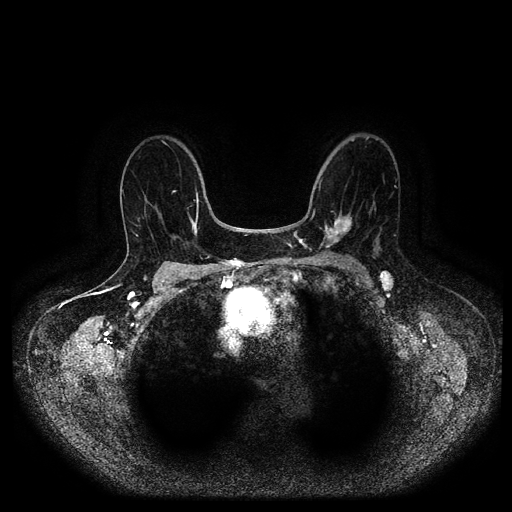
Breast MRI (dynamic contrast-enhanced, multi-phase), one axial slice. Position 59 of 116 along the scan axis. Dynamic contrast-enhanced series, time point 2 of 5 at this slice position (early post-contrast). 1.5 T. TE 2.6 ms, TR 5.2 ms. 2 mm slice thickness. 512 × 512 image matrix, field of view 380 × 380 mm. Female patient, age 69 years.
Outlined on this slice (semi-automatically segmented with operator editing):
- breast lesion (labelled 'tumour' in the annotation; benign lesions carry a separate 'benign' label): bounding box <319,210,358,253> (left, top, right, bottom; pixels)